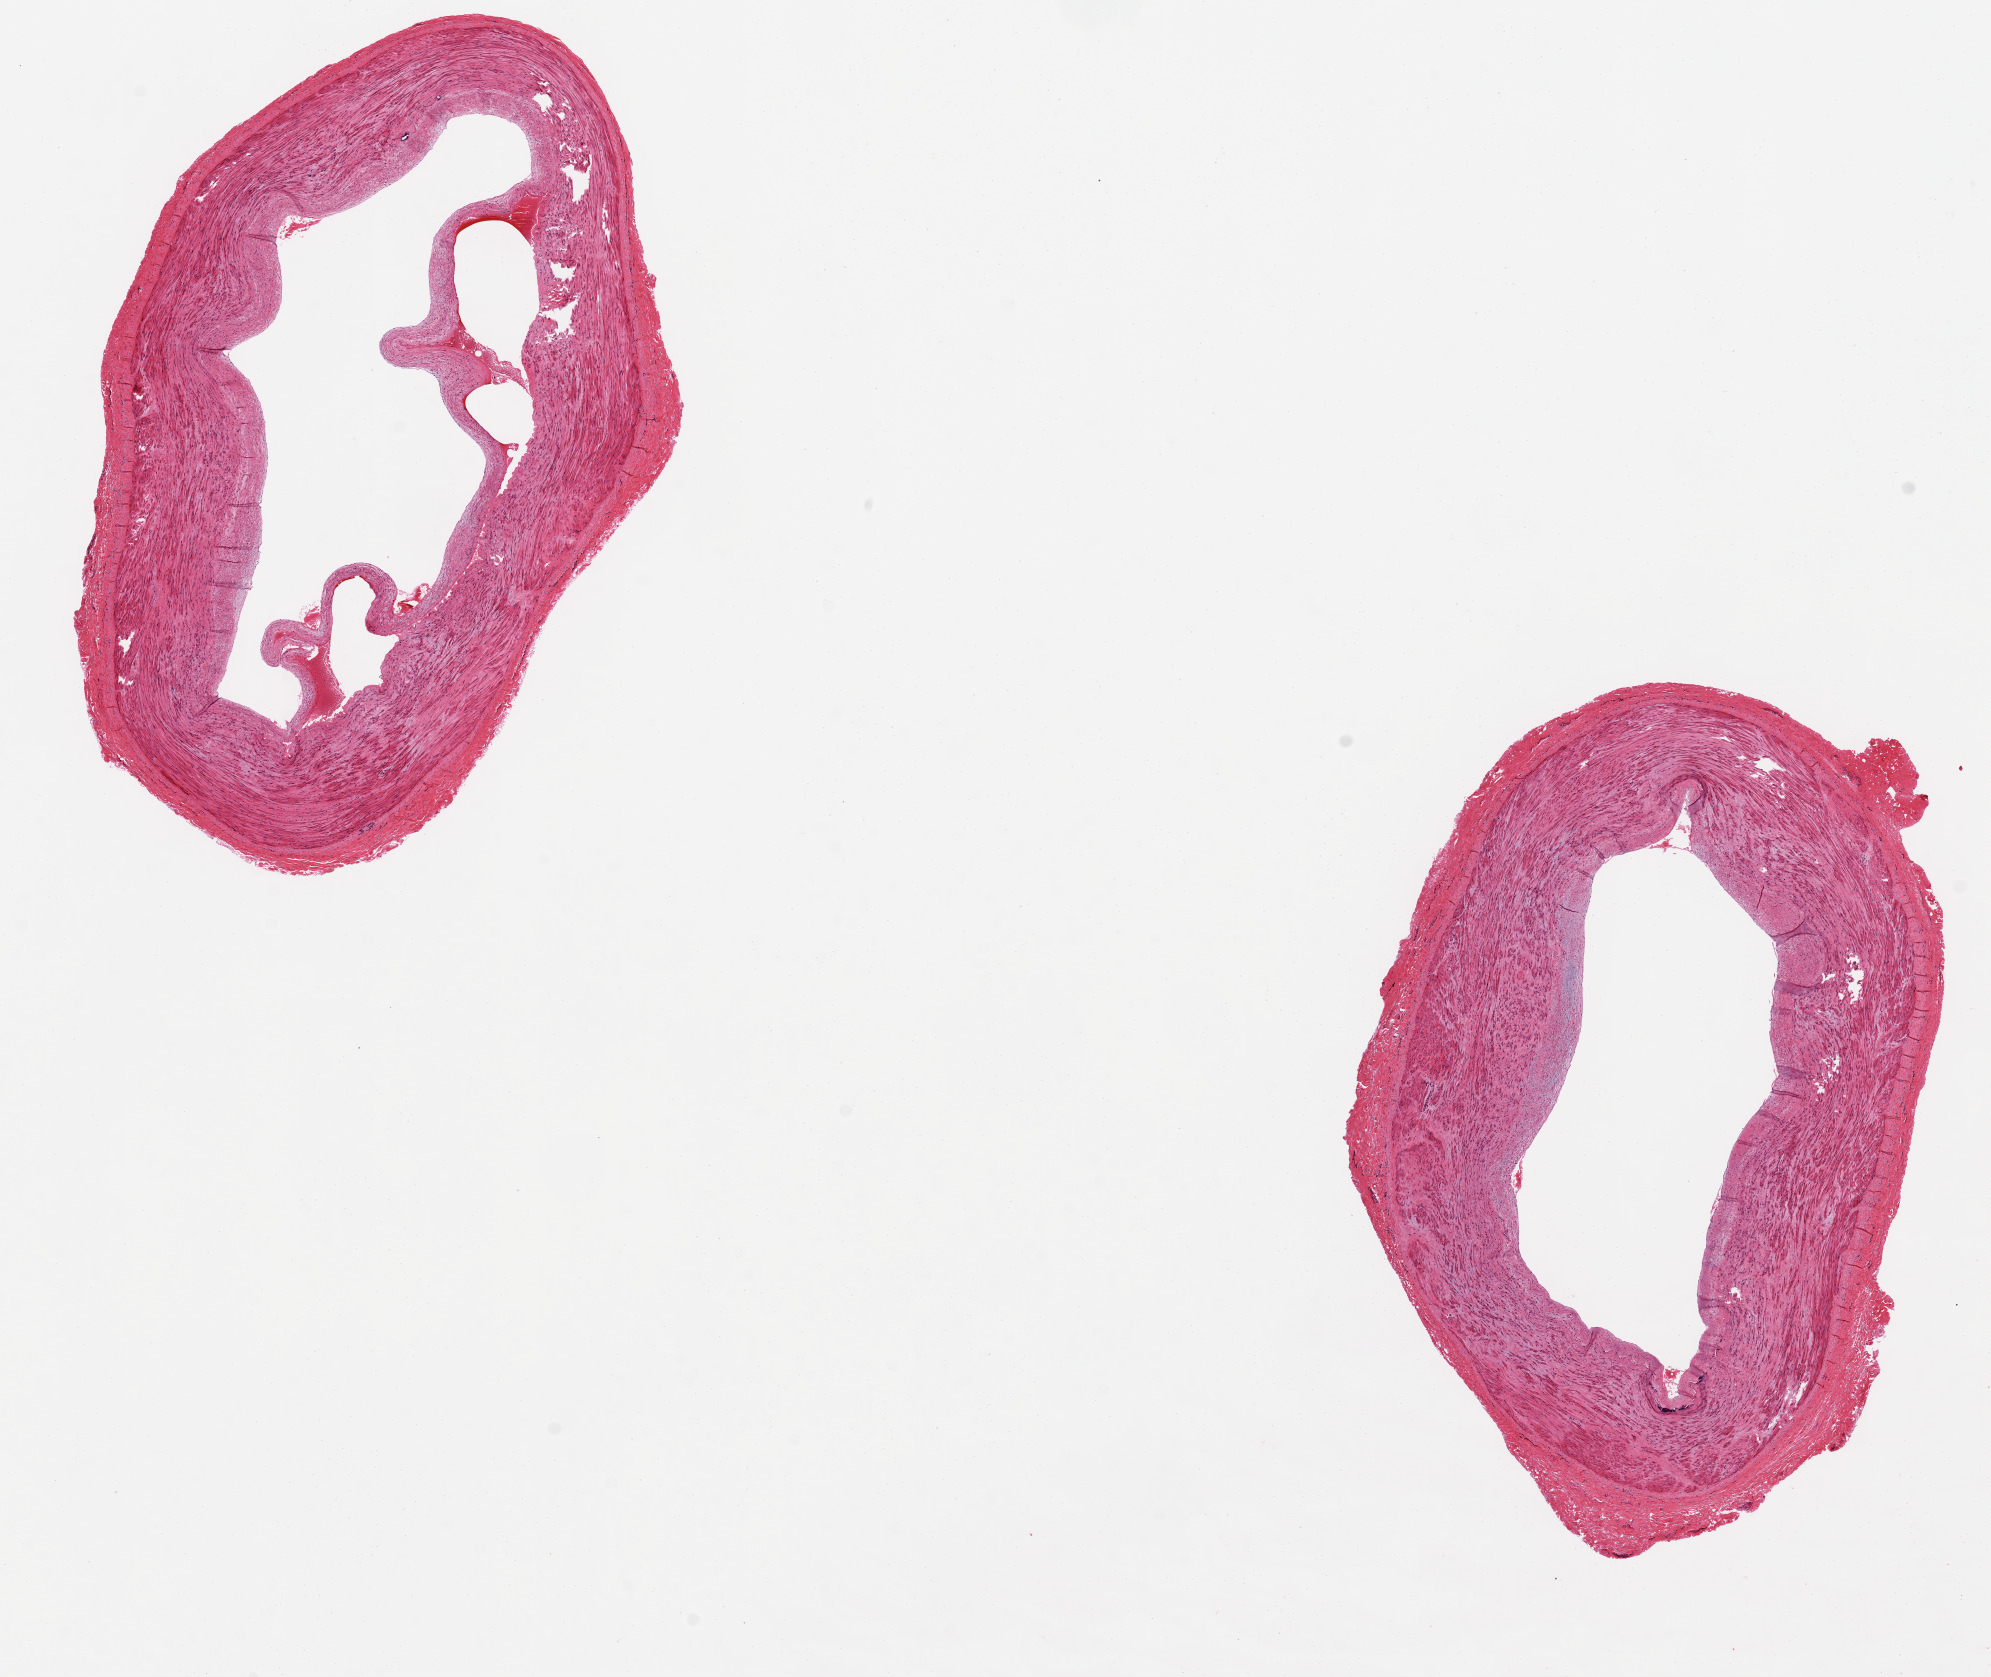
H&E whole-slide image — shown as a low-resolution overview of the whole scanned area (about 15.8 x 13.3 mm, slide scanned at 20x), PAXgene-fixed paraffin-embedded (PFPE) section, sampled site (target tissue): tibial artery, donor tissue sample. Male donor.
Pathologist's review note for this sample: 4.4 x 6.8 mm specimen.